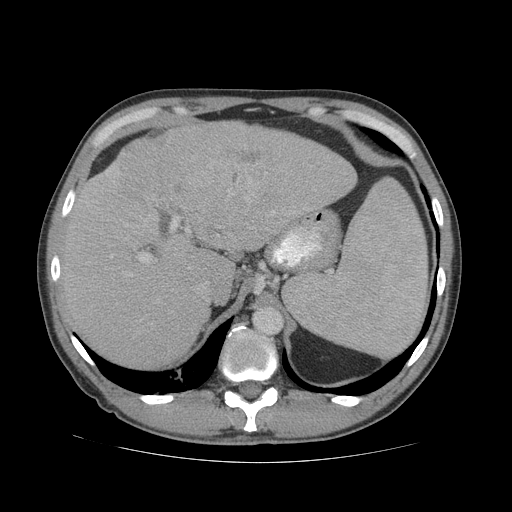
Contrast-enhanced abdominal CT (liver protocol), one axial slice. Slice 50 of 81 in the series (ordered by position). Reconstruction kernel STANDARD. 140 kVp. Soft-tissue window (W 400 / L 40 HU). 2.5 mm slice thickness. 512 × 512 image matrix. Case-level facts recorded for this patient, not image findings: diagnosis: hepatocellular carcinoma (patient treated with transarterial chemoembolisation; whether this scan precedes or follows treatment is not stated here); TNM stage (as recorded): Stage-IVB; Child-Pugh class: B; tumour differentiation: well differentiated.
Outlined on this slice (semi-automatic segmentation, software-assisted and operator-edited):
- liver parenchyma outside the tumour (the mass and vessels are separate outlines, so this box may not span the whole liver): box from (x=60, y=120) to (x=356, y=368) px
- mass: (x=107, y=119)–(x=270, y=223)
- liver vessels: (x=106, y=167)–(x=295, y=262)